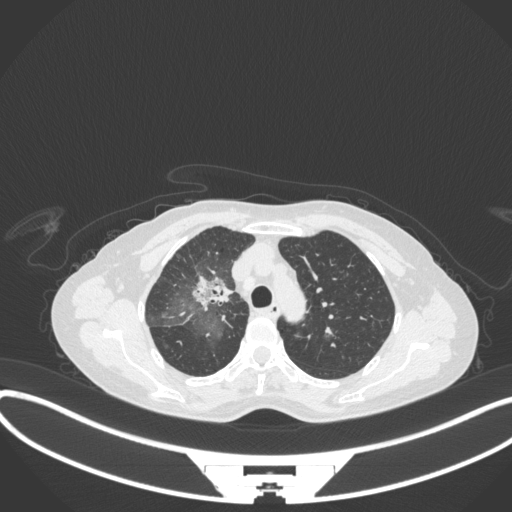
Chest CT, one axial slice; slice 238 of 311 in the series (ordered by position); reconstruction kernel B31f; lung window (W 1500 / L -600 HU); 512 × 512 image matrix. Female patient, age 59 years. From the clinical record (not read from this slice): clinical TNM (as recorded): T3 N0 M0.
Annotated regions visible in this slice (rectangle marked by the reading radiologist):
- lung tumour (recorded histology: adenocarcinoma): box from (x=192, y=276) to (x=235, y=317) px